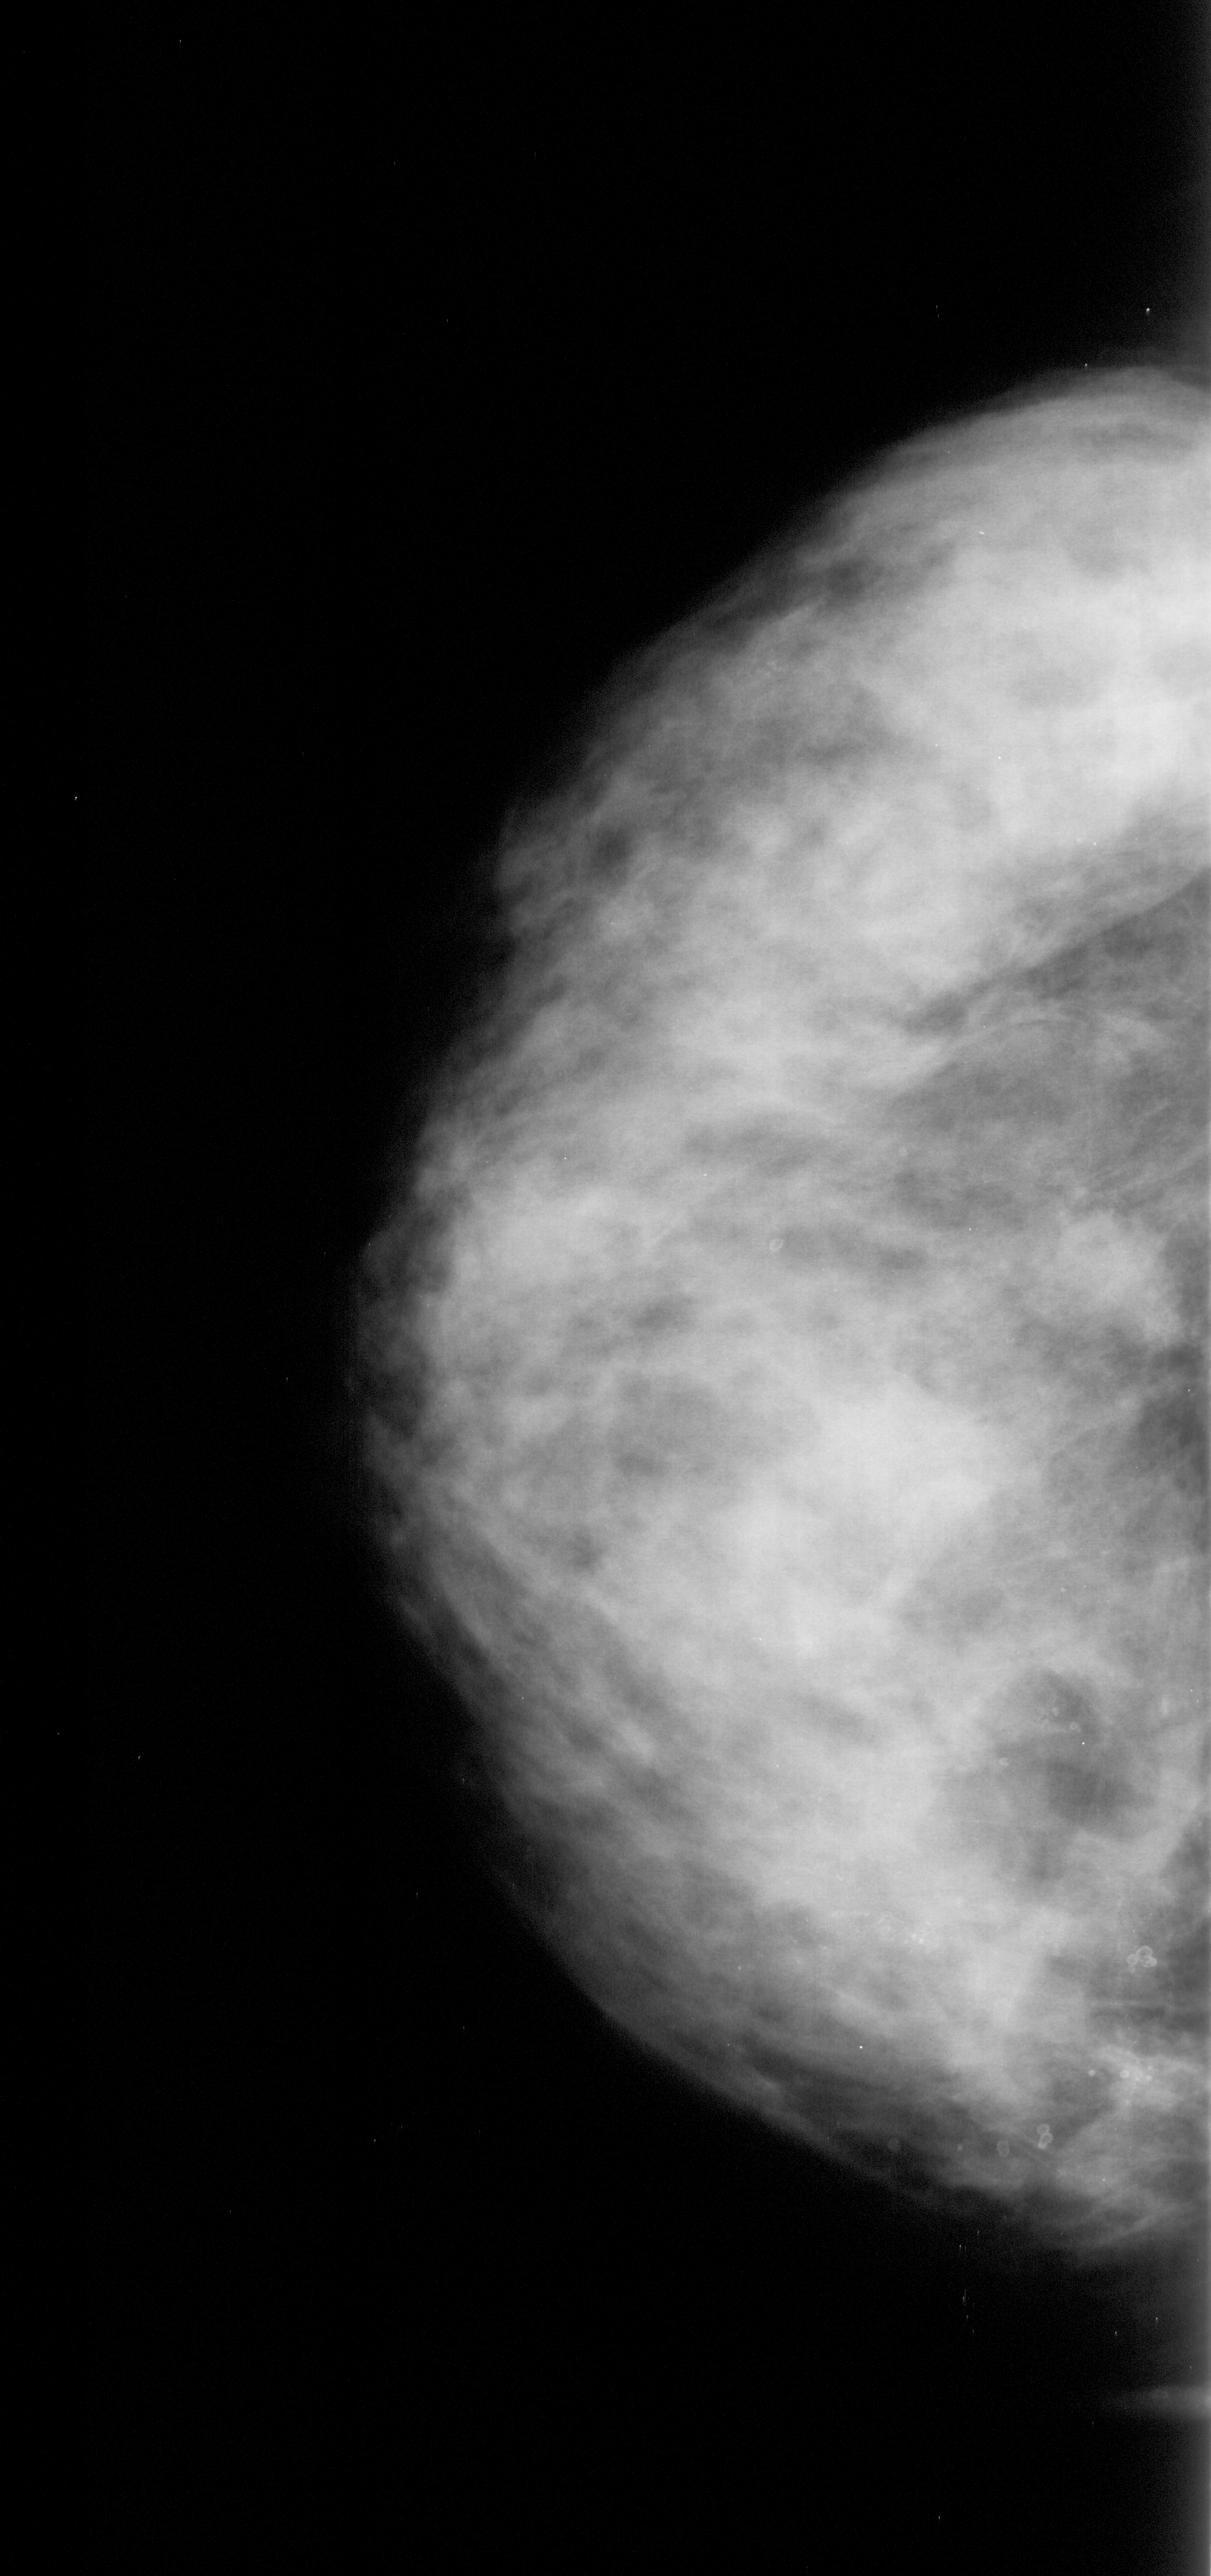
Mammogram (digitized film); left breast; craniocaudal (CC) view; BI-RADS breast density category 3 (scale 1–4); 1211 × 2576 image matrix.
Expert-marked regions of interest on this film, with their recorded descriptors:
- calcifications, morphology pleomorphic, distribution clustered; BI-RADS assessment category 4; pathology result (as recorded, not read from the image): malignant: bounding box (x1, y1, x2, y2) in pixels: (756, 1884, 1174, 2008)